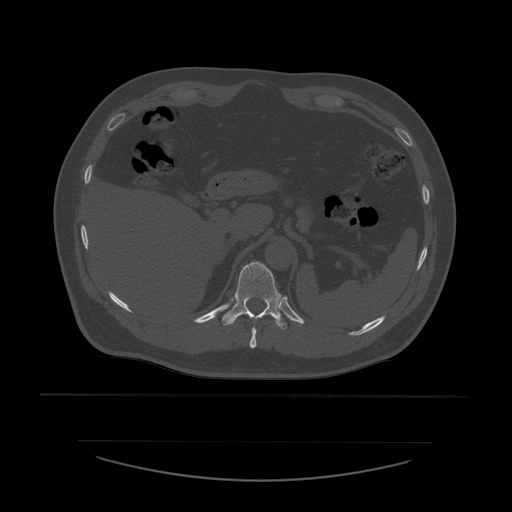
CT including the spine, one axial slice; position 280 of 532 along the scan axis; reconstruction kernel STANDARD; 120 kVp; bone window (W 1800 / L 400 HU); 512 × 512 image matrix, field of view 441 × 441 mm. Patient age 44 years. From the clinical record (not read from this slice): primary cancer: soft tissue sarcoma.
Structures marked on this image (semi-automatically segmented with operator editing):
- T10 vertebra: bounding box <250,327,257,349> (left, top, right, bottom; pixels)
- T11 vertebra: <222,262,287,330>